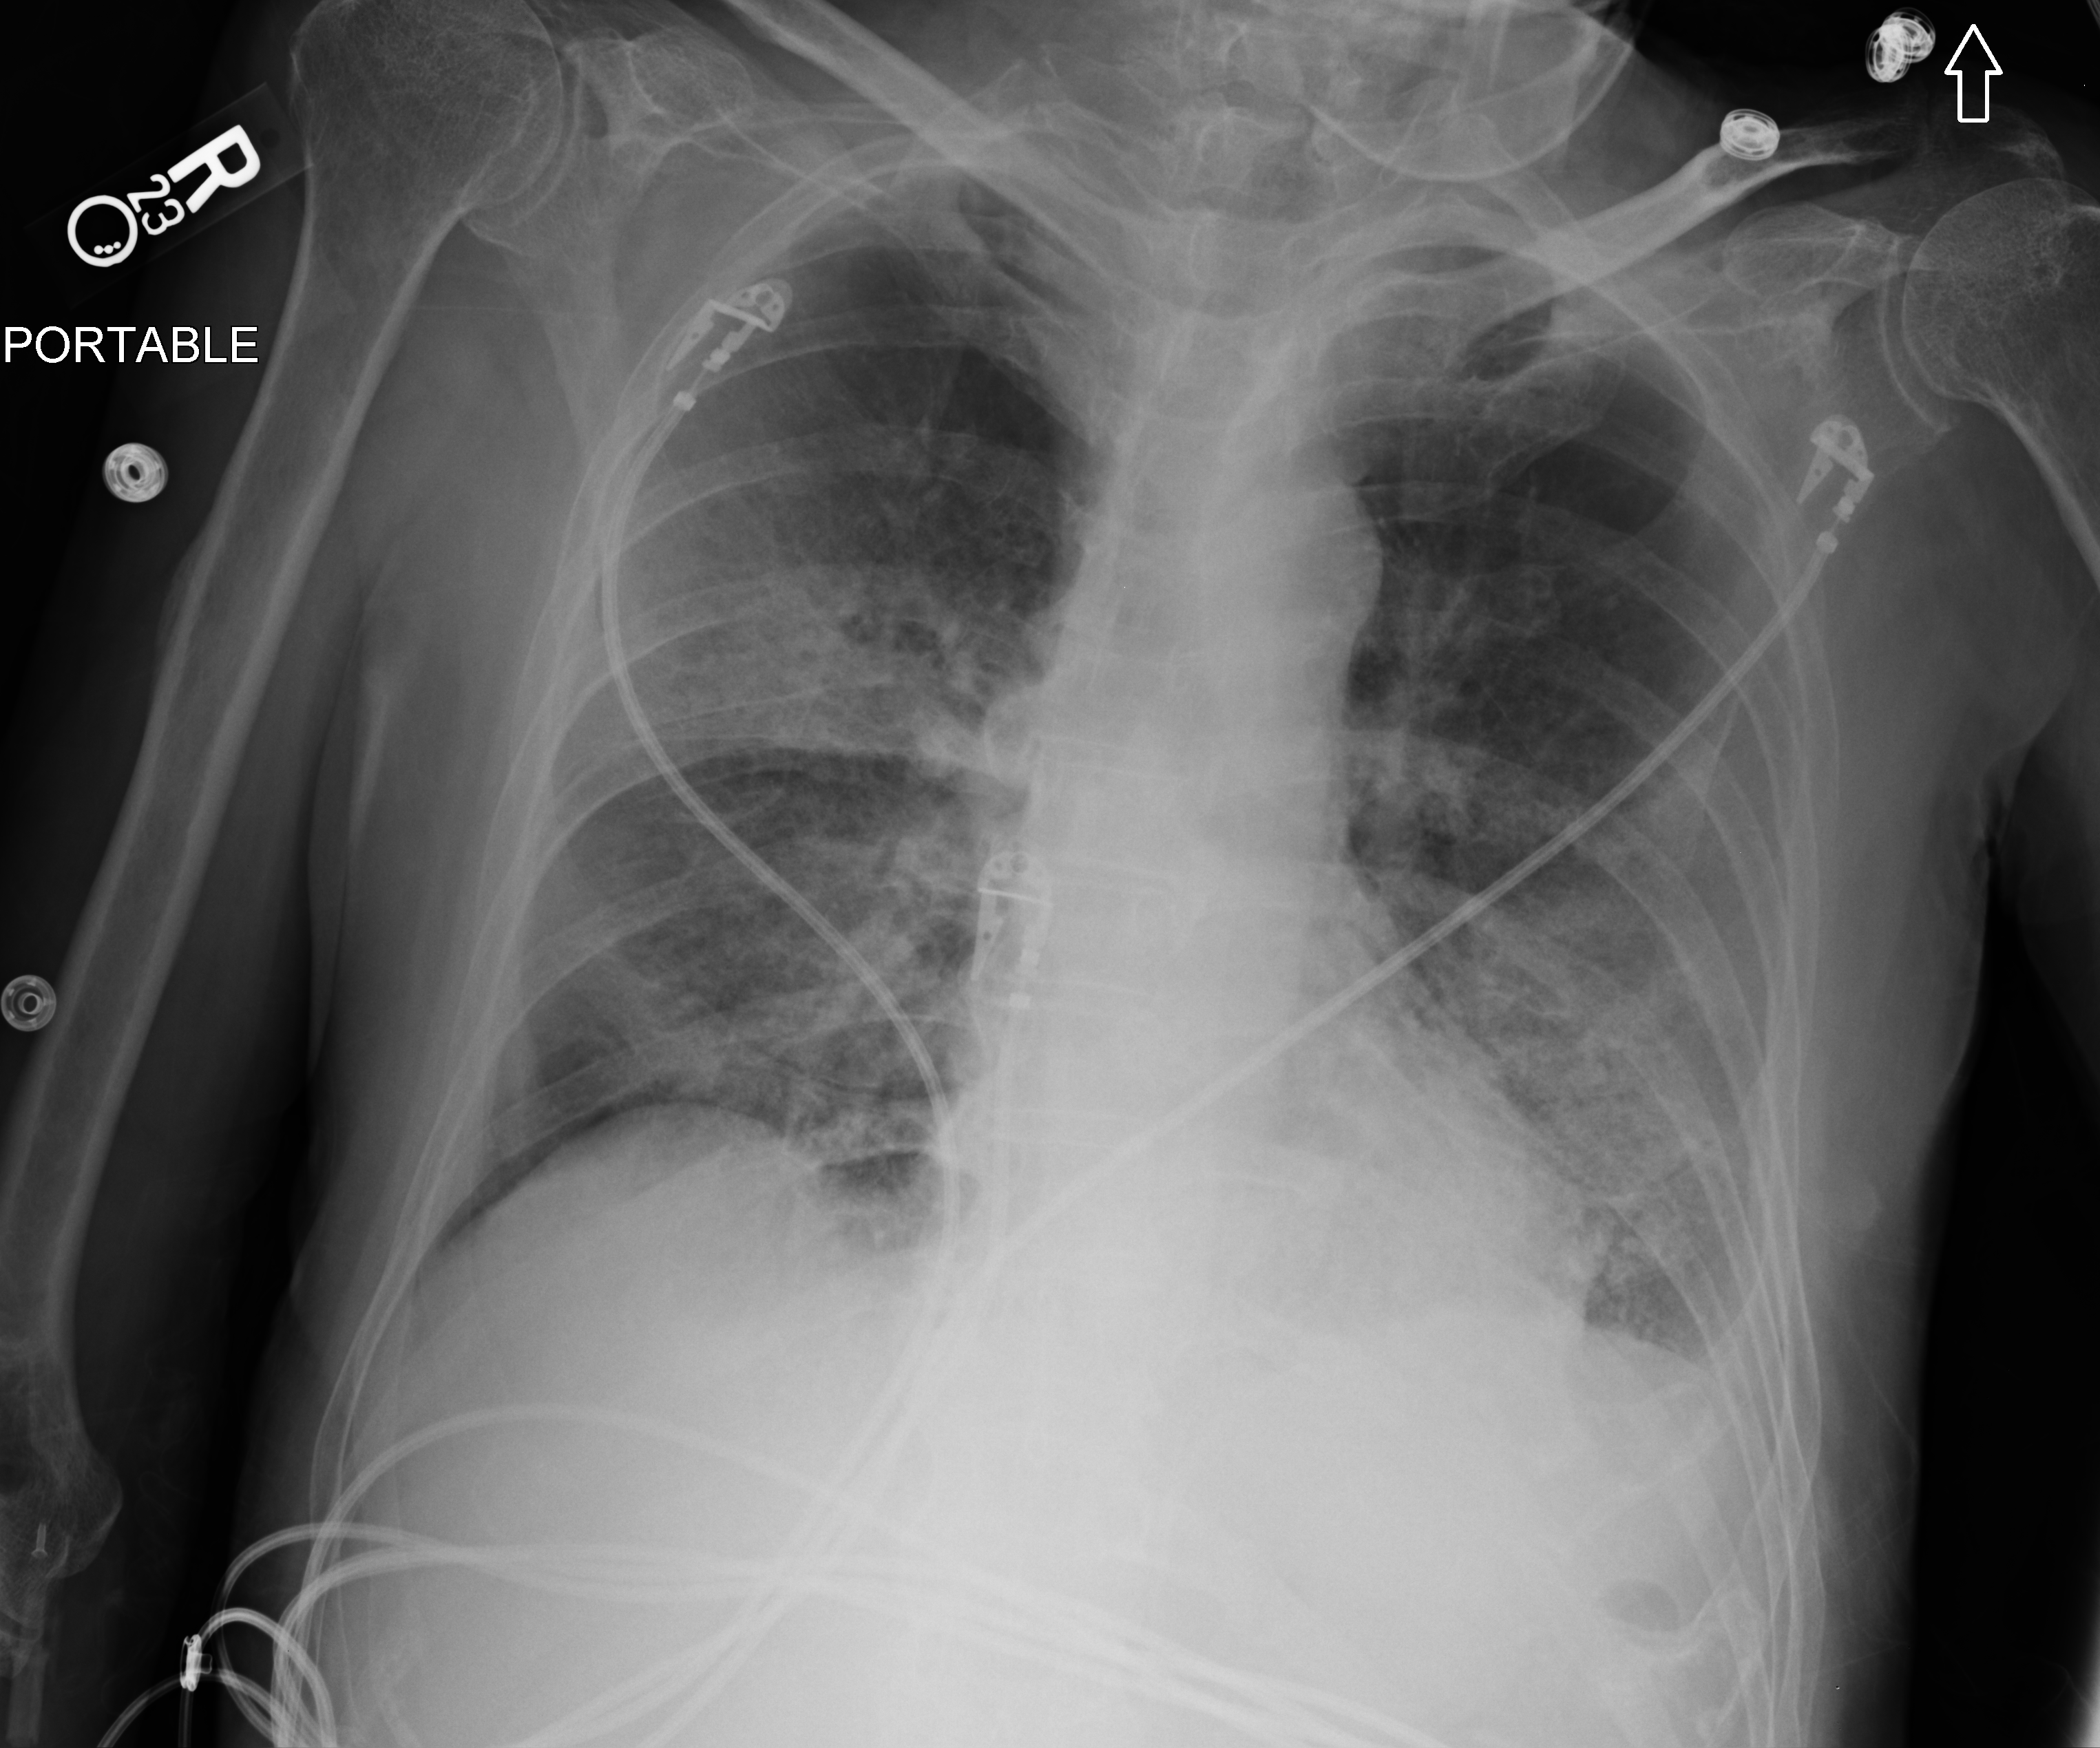
Portable chest radiograph, anteroposterior (AP) projection. Male patient hospitalised with COVID-19, age 60–74 years.
Hospital-stay facts (about this admission, not read from this image; timing relative to this image not recorded): COPD (admission record): no; admitted to intensive care during this hospital stay: yes.